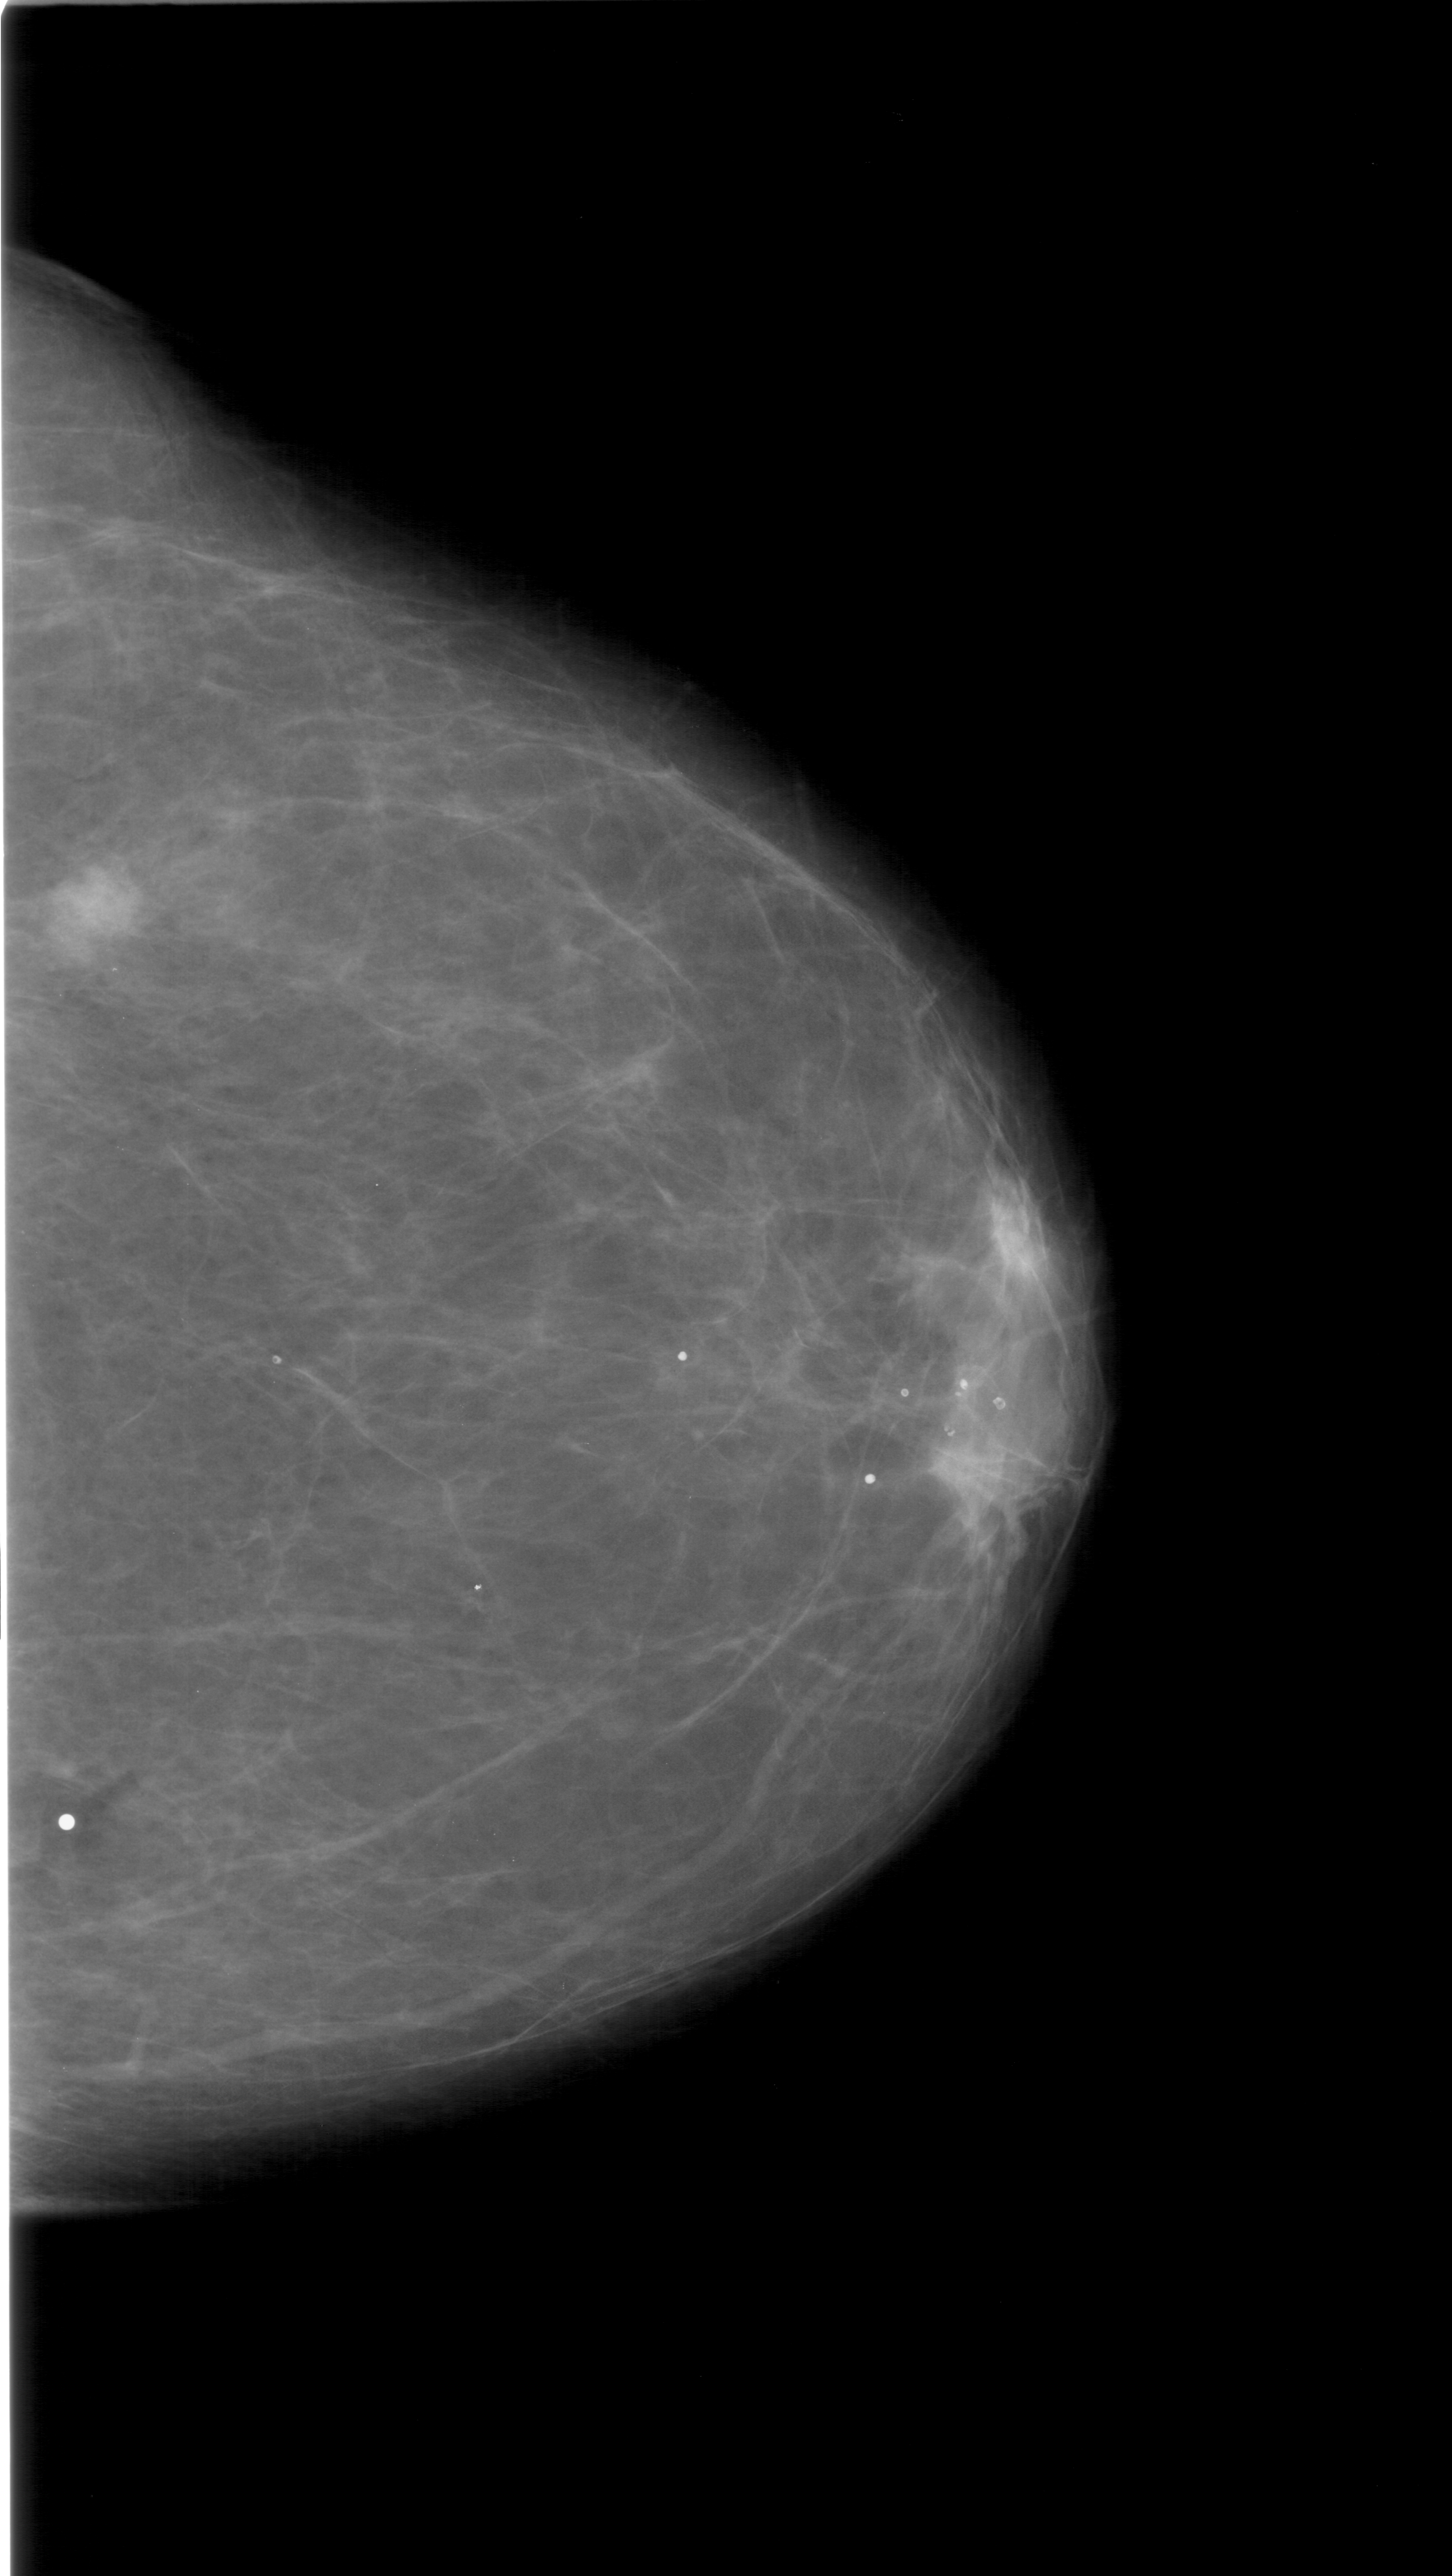
Mammogram (digitized film). Right breast. CC view. Breast composition: almost entirely fatty (BI-RADS density category 1 of 4). 1452 × 2576 image matrix.
Marked abnormalities (boxes around the expert regions of interest):
- mass, shape irregular, margins ill defined; BI-RADS assessment category 5; pathology (as recorded): malignant: bounding box [x1, y1, x2, y2] px = [45, 856, 147, 945]